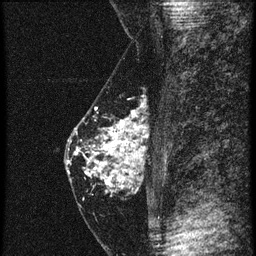
Breast MRI (dynamic contrast-enhanced), one sagittal slice; position 23 of 60 along the scan axis; 4 images stored at this slice position (order not interpretable as contrast timing); 1.5 T; TE 4.2 ms, TR 20.4 ms; 256 × 256 image matrix, field of view 180 × 180 mm. Female patient, age 46 years. Case-level facts recorded for this patient, not image findings: setting: breast cancer imaged before/during neoadjuvant chemotherapy; receptor status: triple-negative.
Outlined on this slice (semi-automatically segmented with operator editing):
- analysis volume of interest (the breast-tissue region the enhancement analysis was run in; not a lesion): box from (x=67, y=82) to (x=146, y=201) px
- tumour enhancement mask (voxels above the 90 % enhancement threshold inside the analysis volume of interest): (x=67, y=112)–(x=144, y=189)